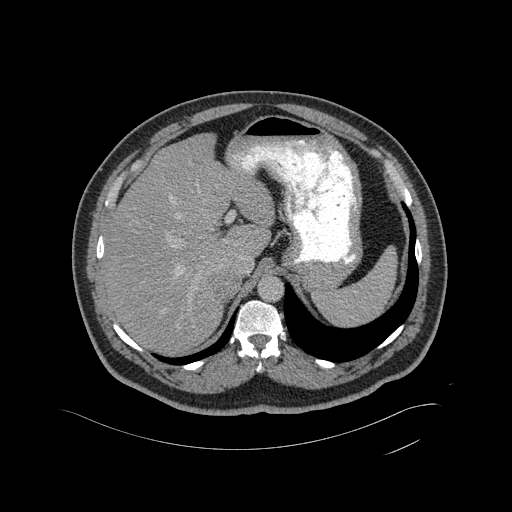
Contrast-enhanced abdominal CT, one axial slice; slice 345 of 433 in the series (ordered by position); intravenous contrast given; soft-tissue window (W 400 / L 40 HU); 512 × 512 image matrix, field of view 500 × 500 mm. Patient: male, 56 years. From the clinical record (not read from this slice): diagnosis: adrenocortical carcinoma; tumour side: right adrenal; tumour size at pathology: 11.6 cm; Ki-67 index: 50 %; stage (as recorded): 3.
Structures marked on this image (semi-automatic segmentation, software-assisted and operator-edited):
- mass: box from (x=212, y=271) to (x=238, y=299) px